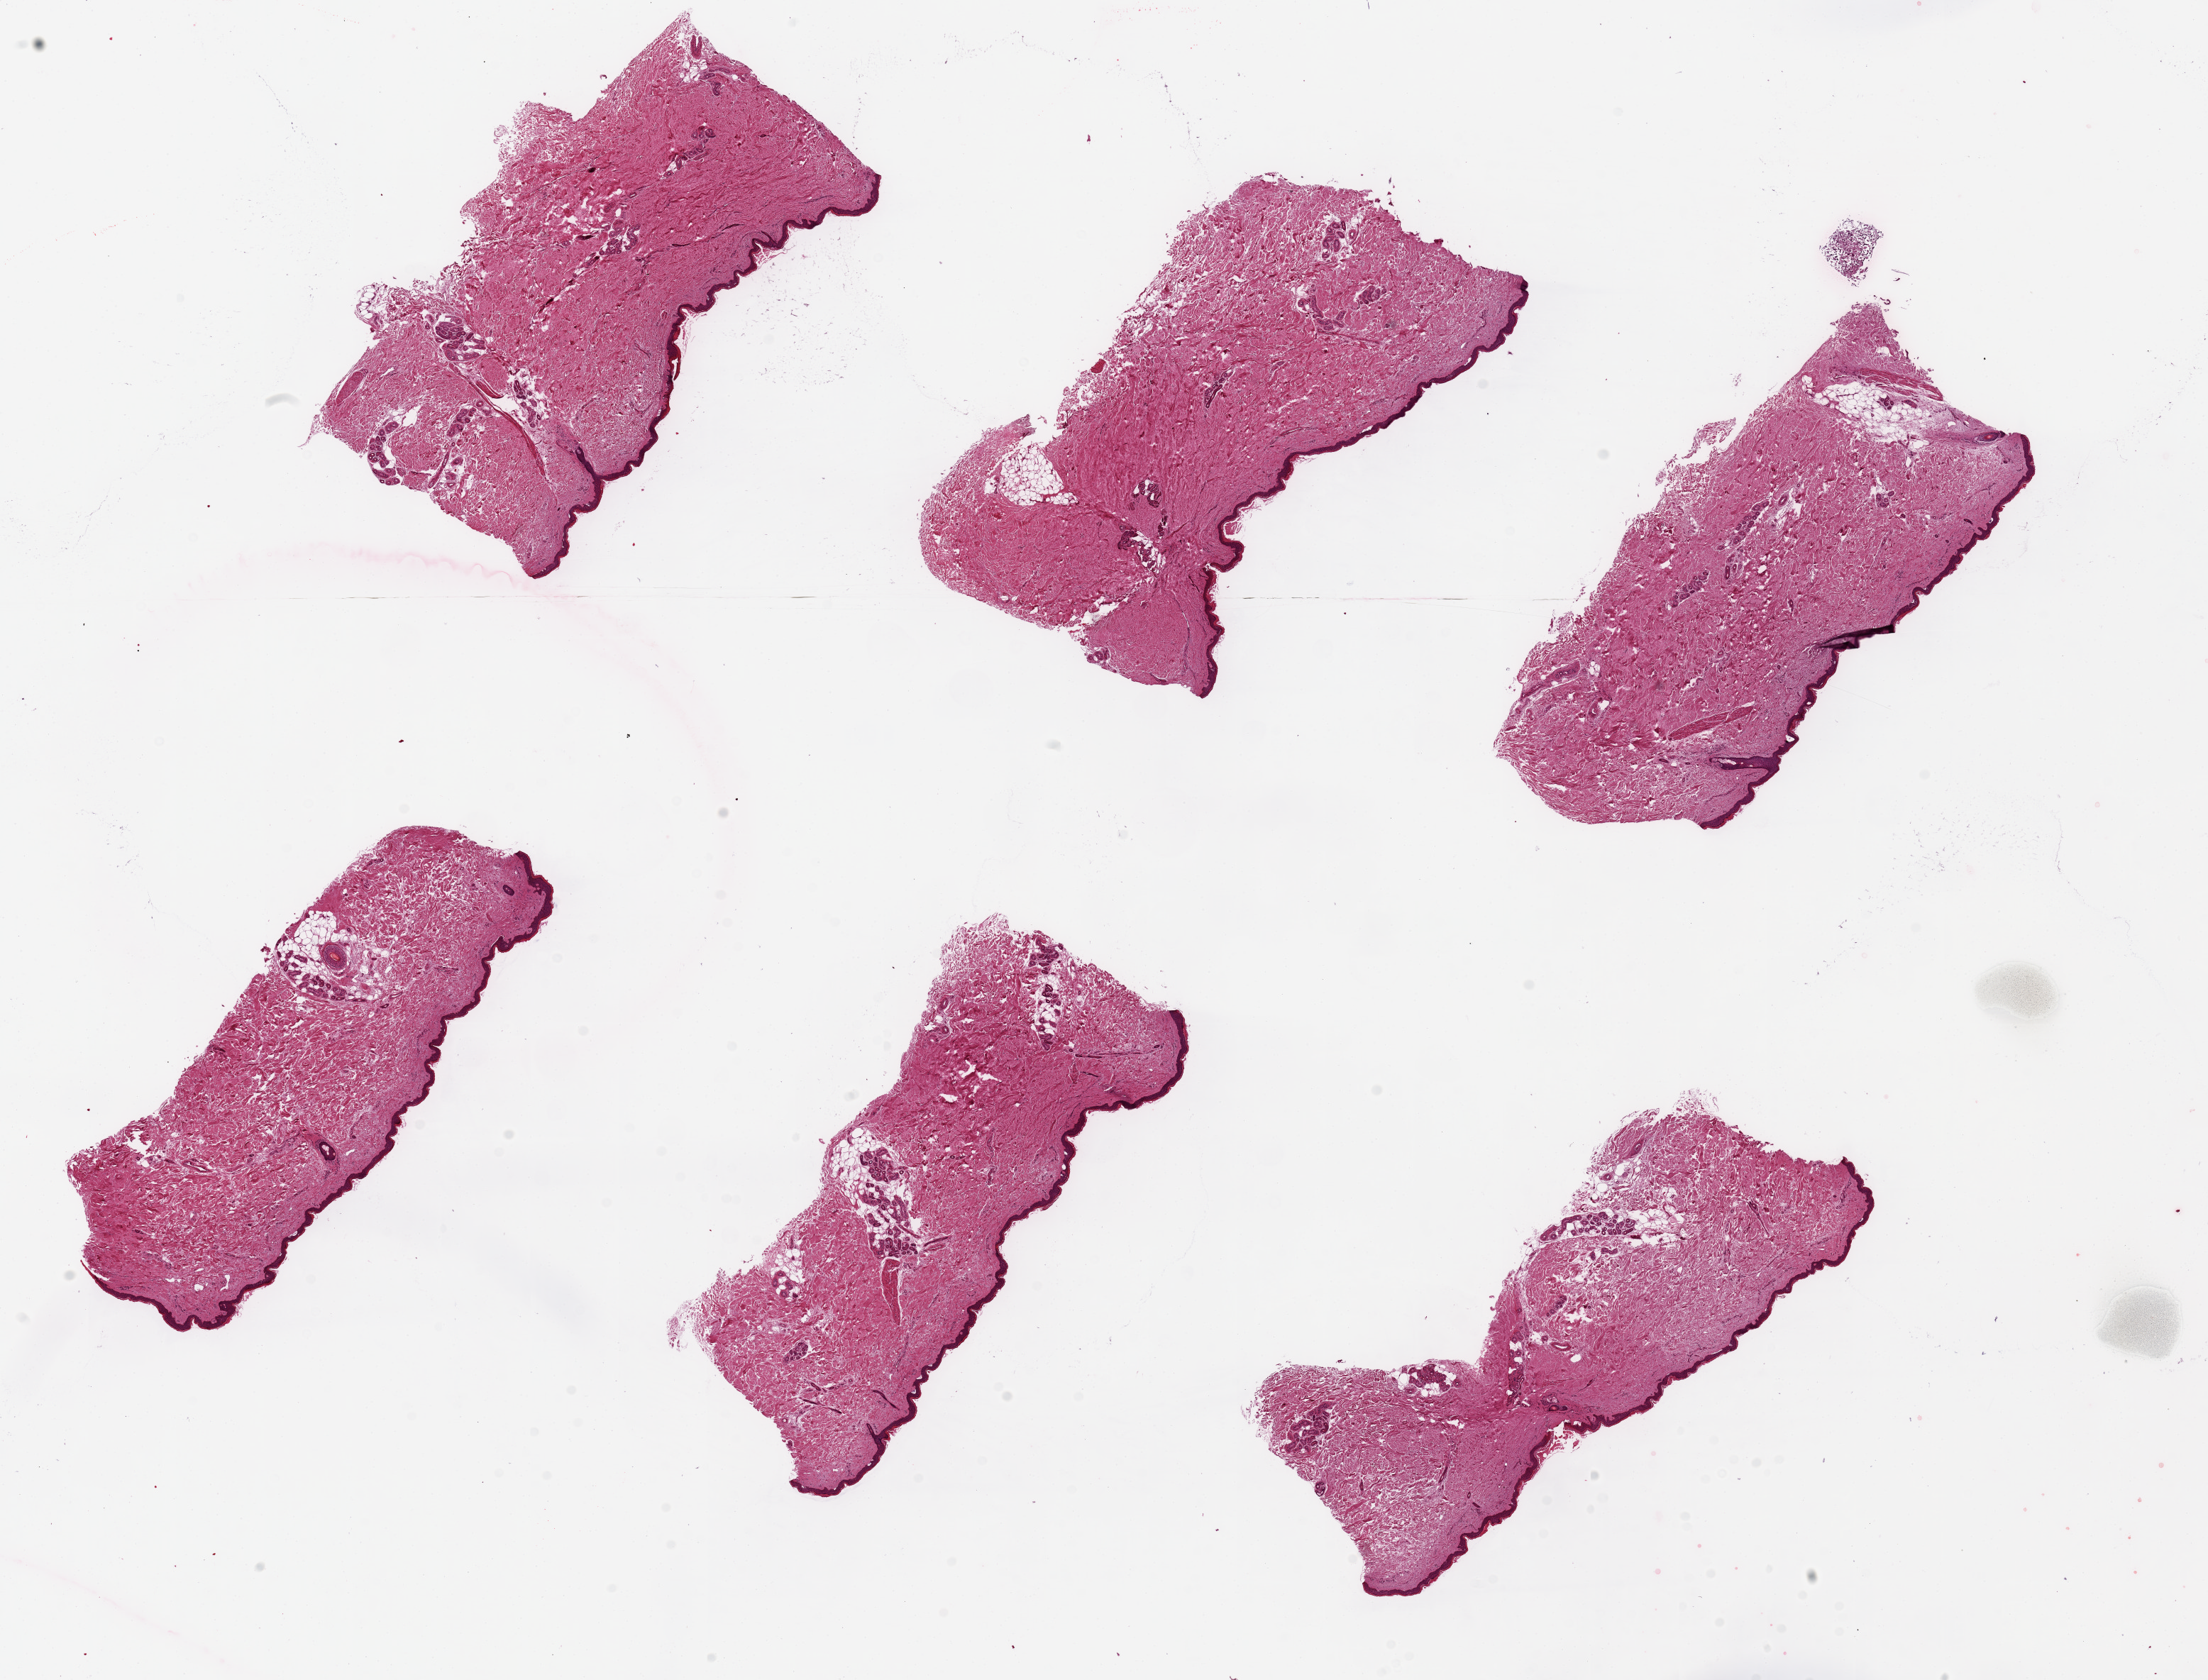
Whole-slide image, hematoxylin and eosin (H&E) stain, whole scanned area (about 24.6 x 18.7 mm, slide scanned at 20x) shown as a low-resolution overview; PAXgene-fixed, paraffin-embedded tissue; sampled site (target tissue): skin of lower leg; donor tissue sample.
Review note (as recorded): 6 pieces, up to 7x3mm; well dissected without subcutaneous adipose.